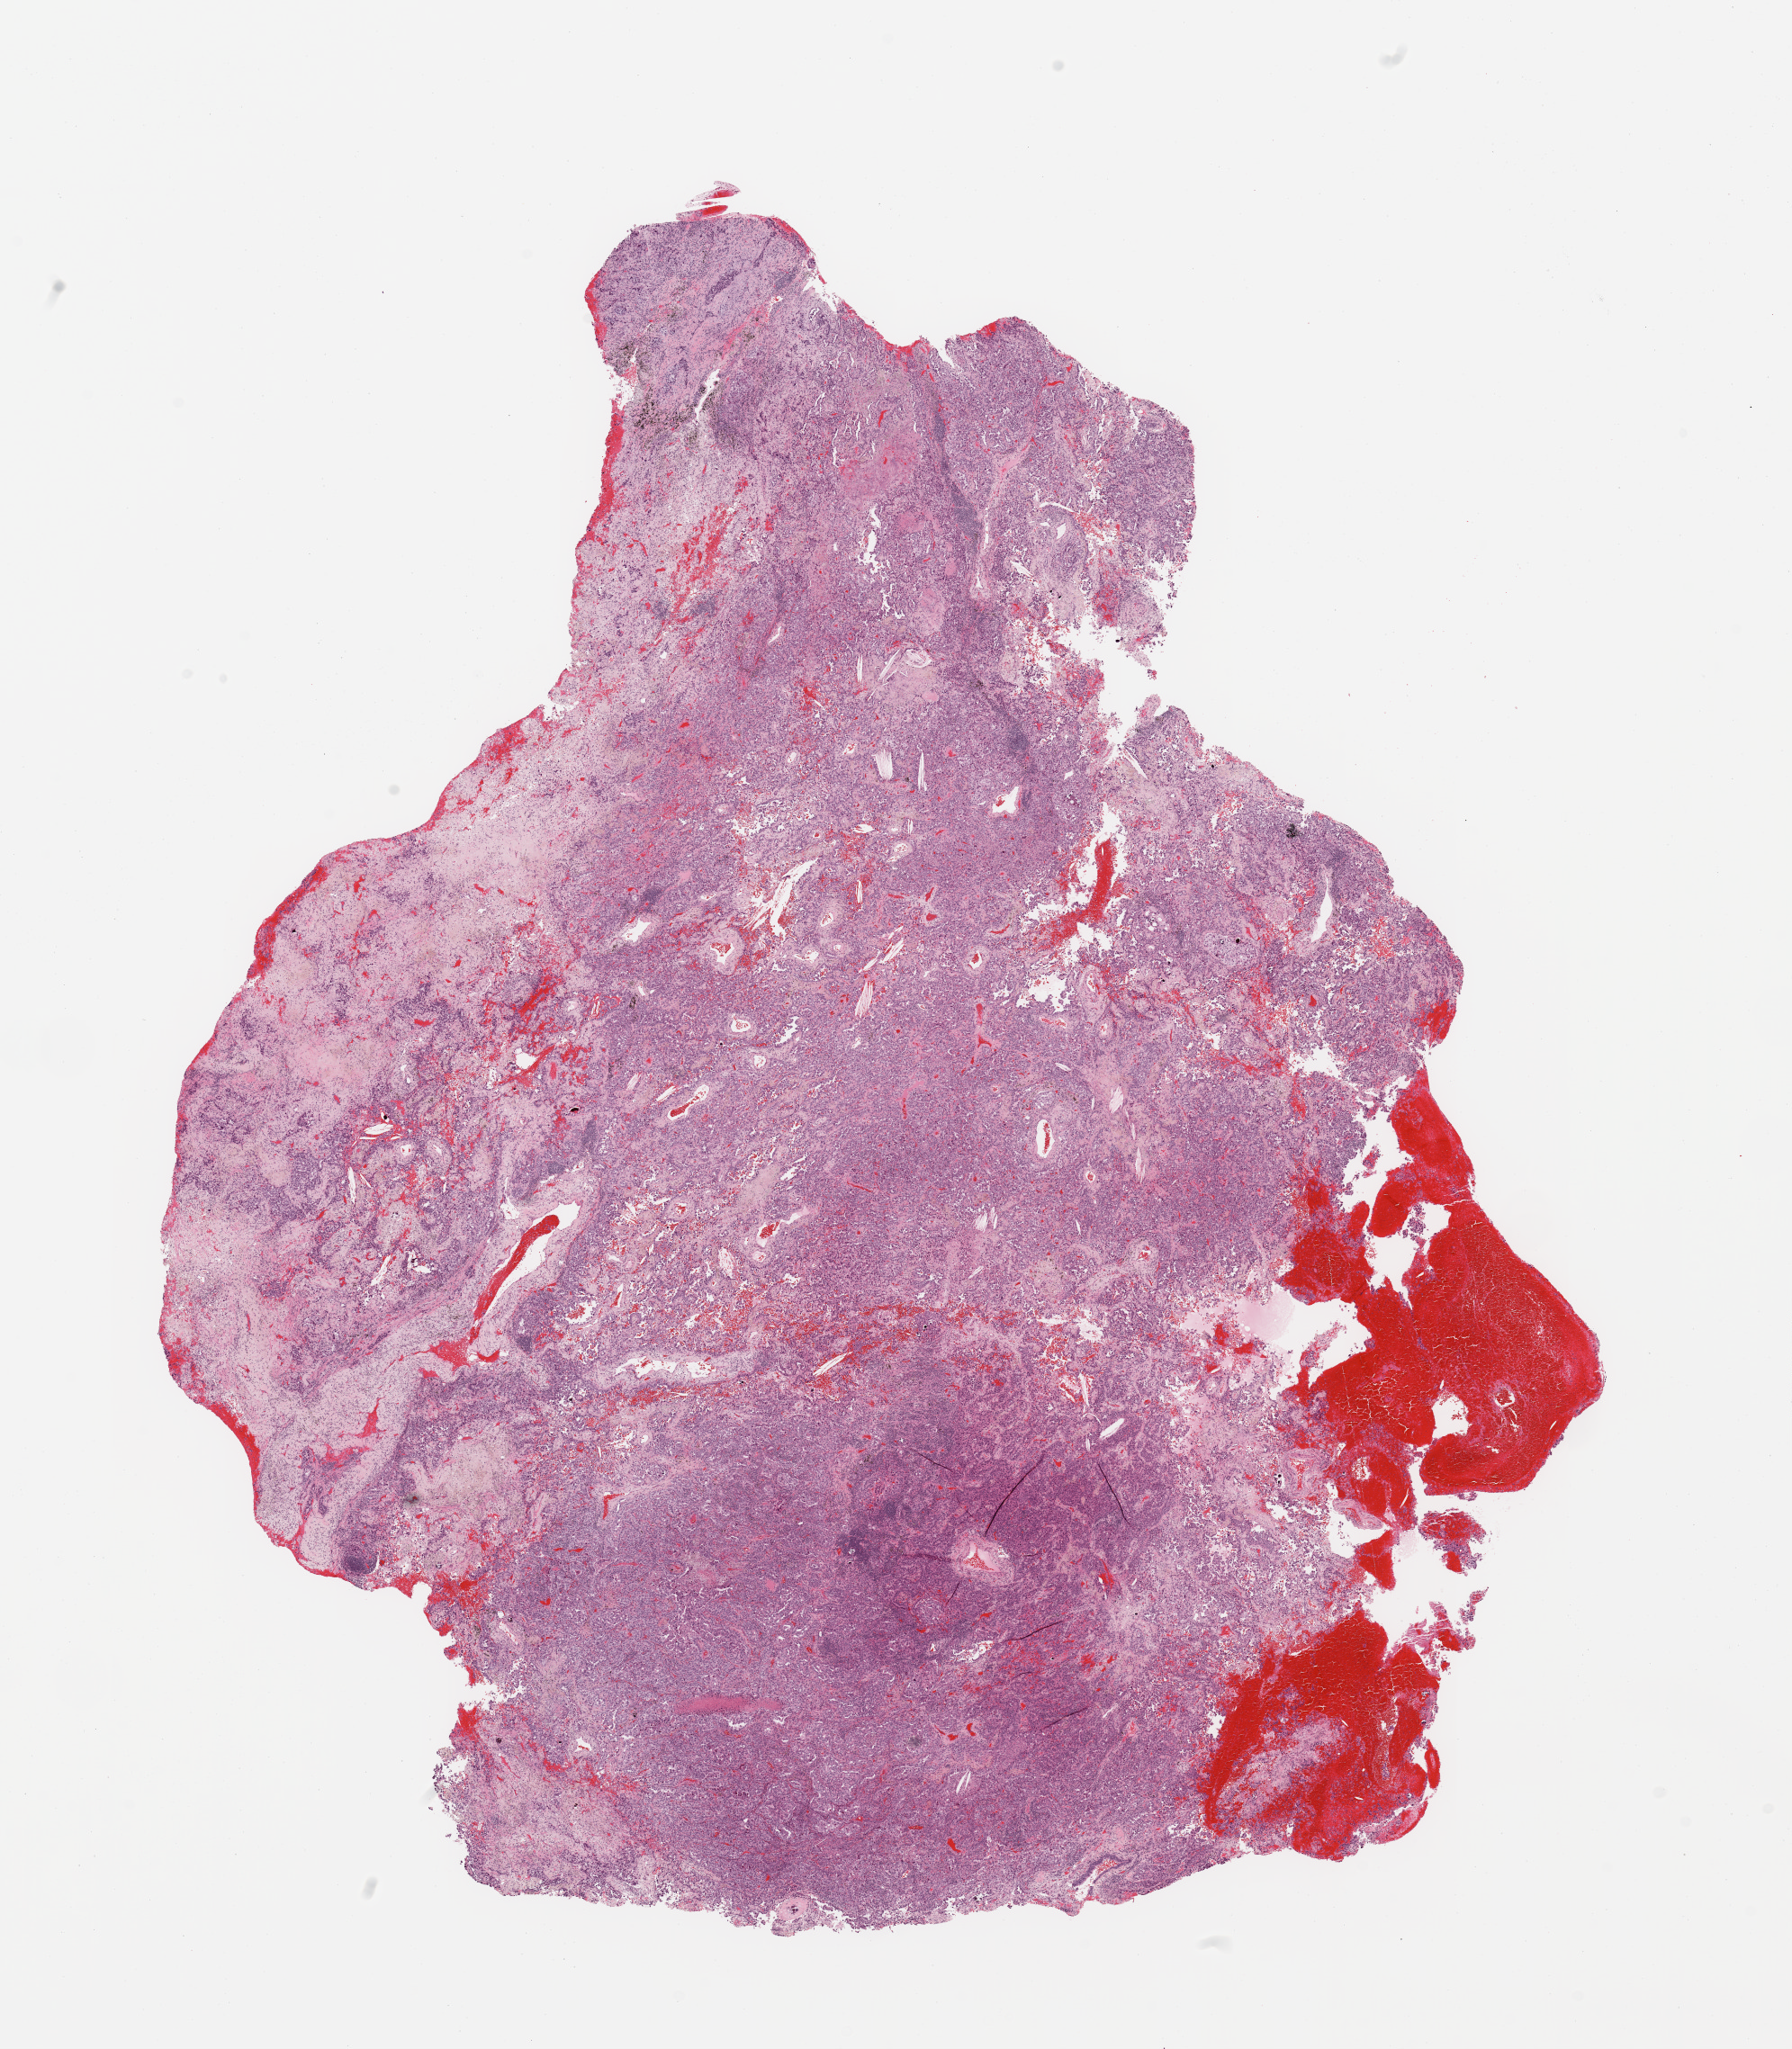
Digitized H&E tissue section (whole slide), low-resolution overview of the scanned area, about 15.8 x 18.0 mm (from a 20x scan). Tumour tissue sample, sampled site: lung. 56-year-old female patient. Histologic grade: G2 (moderately differentiated). Composition of this section per pathologist review: tumour nuclei 70%, necrosis 5%.
AJCC pathologic stage: IIB. Histologic diagnosis: Adenocarcinoma, NOS. Primary tumour site (as recorded): left upper lobe.